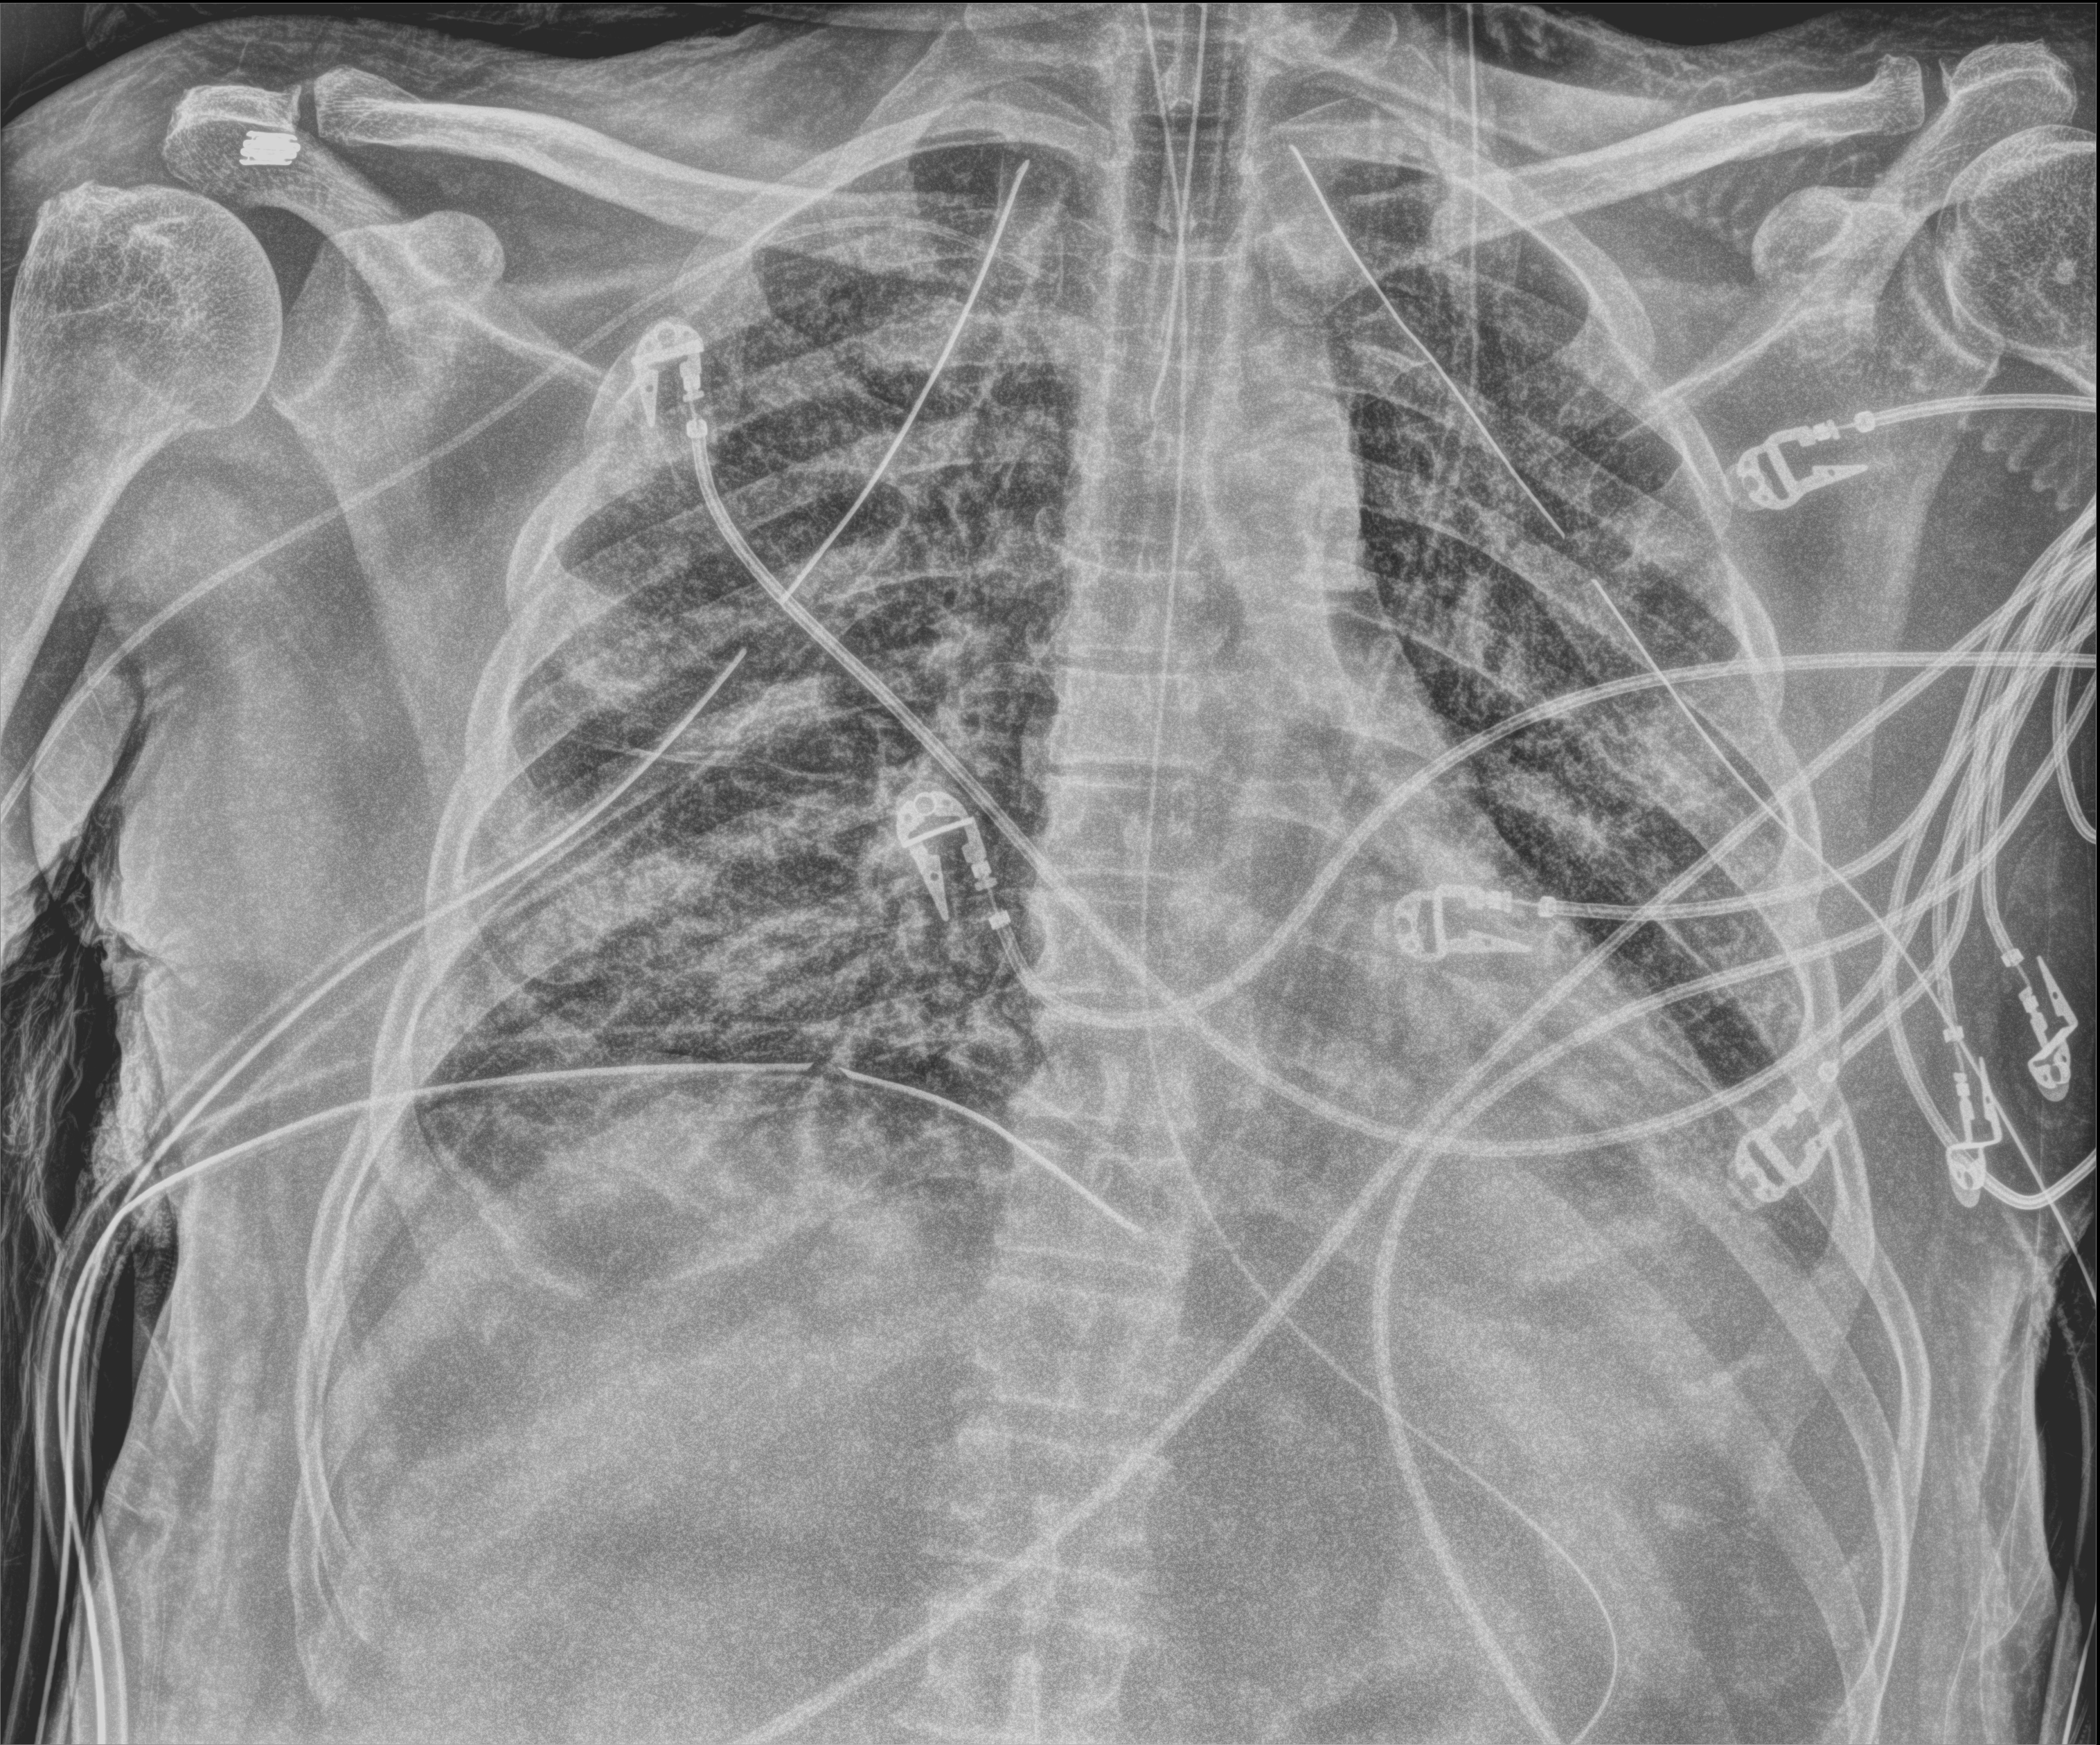
Chest X-ray (portable); anteroposterior (AP) projection. Male patient hospitalised with COVID-19, age 18–59 years.
From the hospital-stay record, not from the radiograph (when in the stay this image was taken is not recorded):
- length of hospital stay: 83 days
- hypertension (admission record): yes